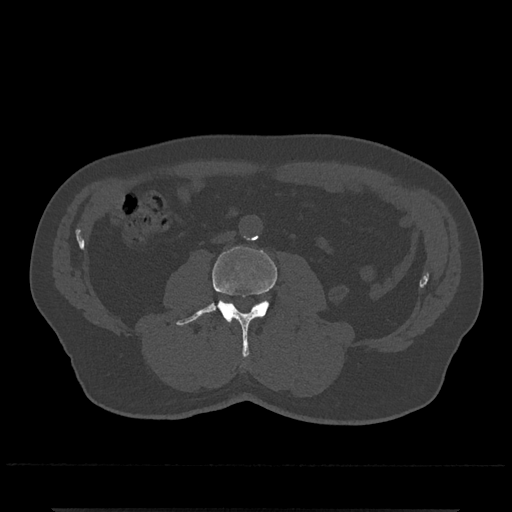
CT including the spine, one axial slice. Position 218 of 797 along the scan axis. Bone window (W 1800 / L 400 HU). 512 × 512 image matrix, field of view 393 × 393 mm. Patient: male, 67 years. Case-level facts recorded for this patient, not image findings: primary cancer: prostate.
Structures marked on this image (semi-automatic segmentation, software-assisted and operator-edited):
- L3 vertebra: bounding box [x1, y1, x2, y2] px = [176, 246, 277, 357]